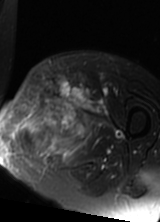
MRI of an extremity soft-tissue mass, one axial slice; position 43 of 69 along the scan axis; T2-weighted fat-saturated; MR volume resampled by the dataset authors to the PET/CT grid (not the native acquisition matrix); 3.27 mm slice thickness; 160 × 222 image matrix, field of view 156 × 217 mm. Female patient. Case-level facts recorded for this patient, not image findings: histological type: pleomorphic leiomyosarcoma; grade: high; site of the primary tumour: left thigh.
Structures marked on this image (expert contour drawn on MRI and transferred to this co-registered scan by the dataset authors):
- gross tumour volume including surrounding oedema: bounding box <16,79,96,162> (left, top, right, bottom; pixels)
- gross tumour volume (mass): <36,79,85,144>